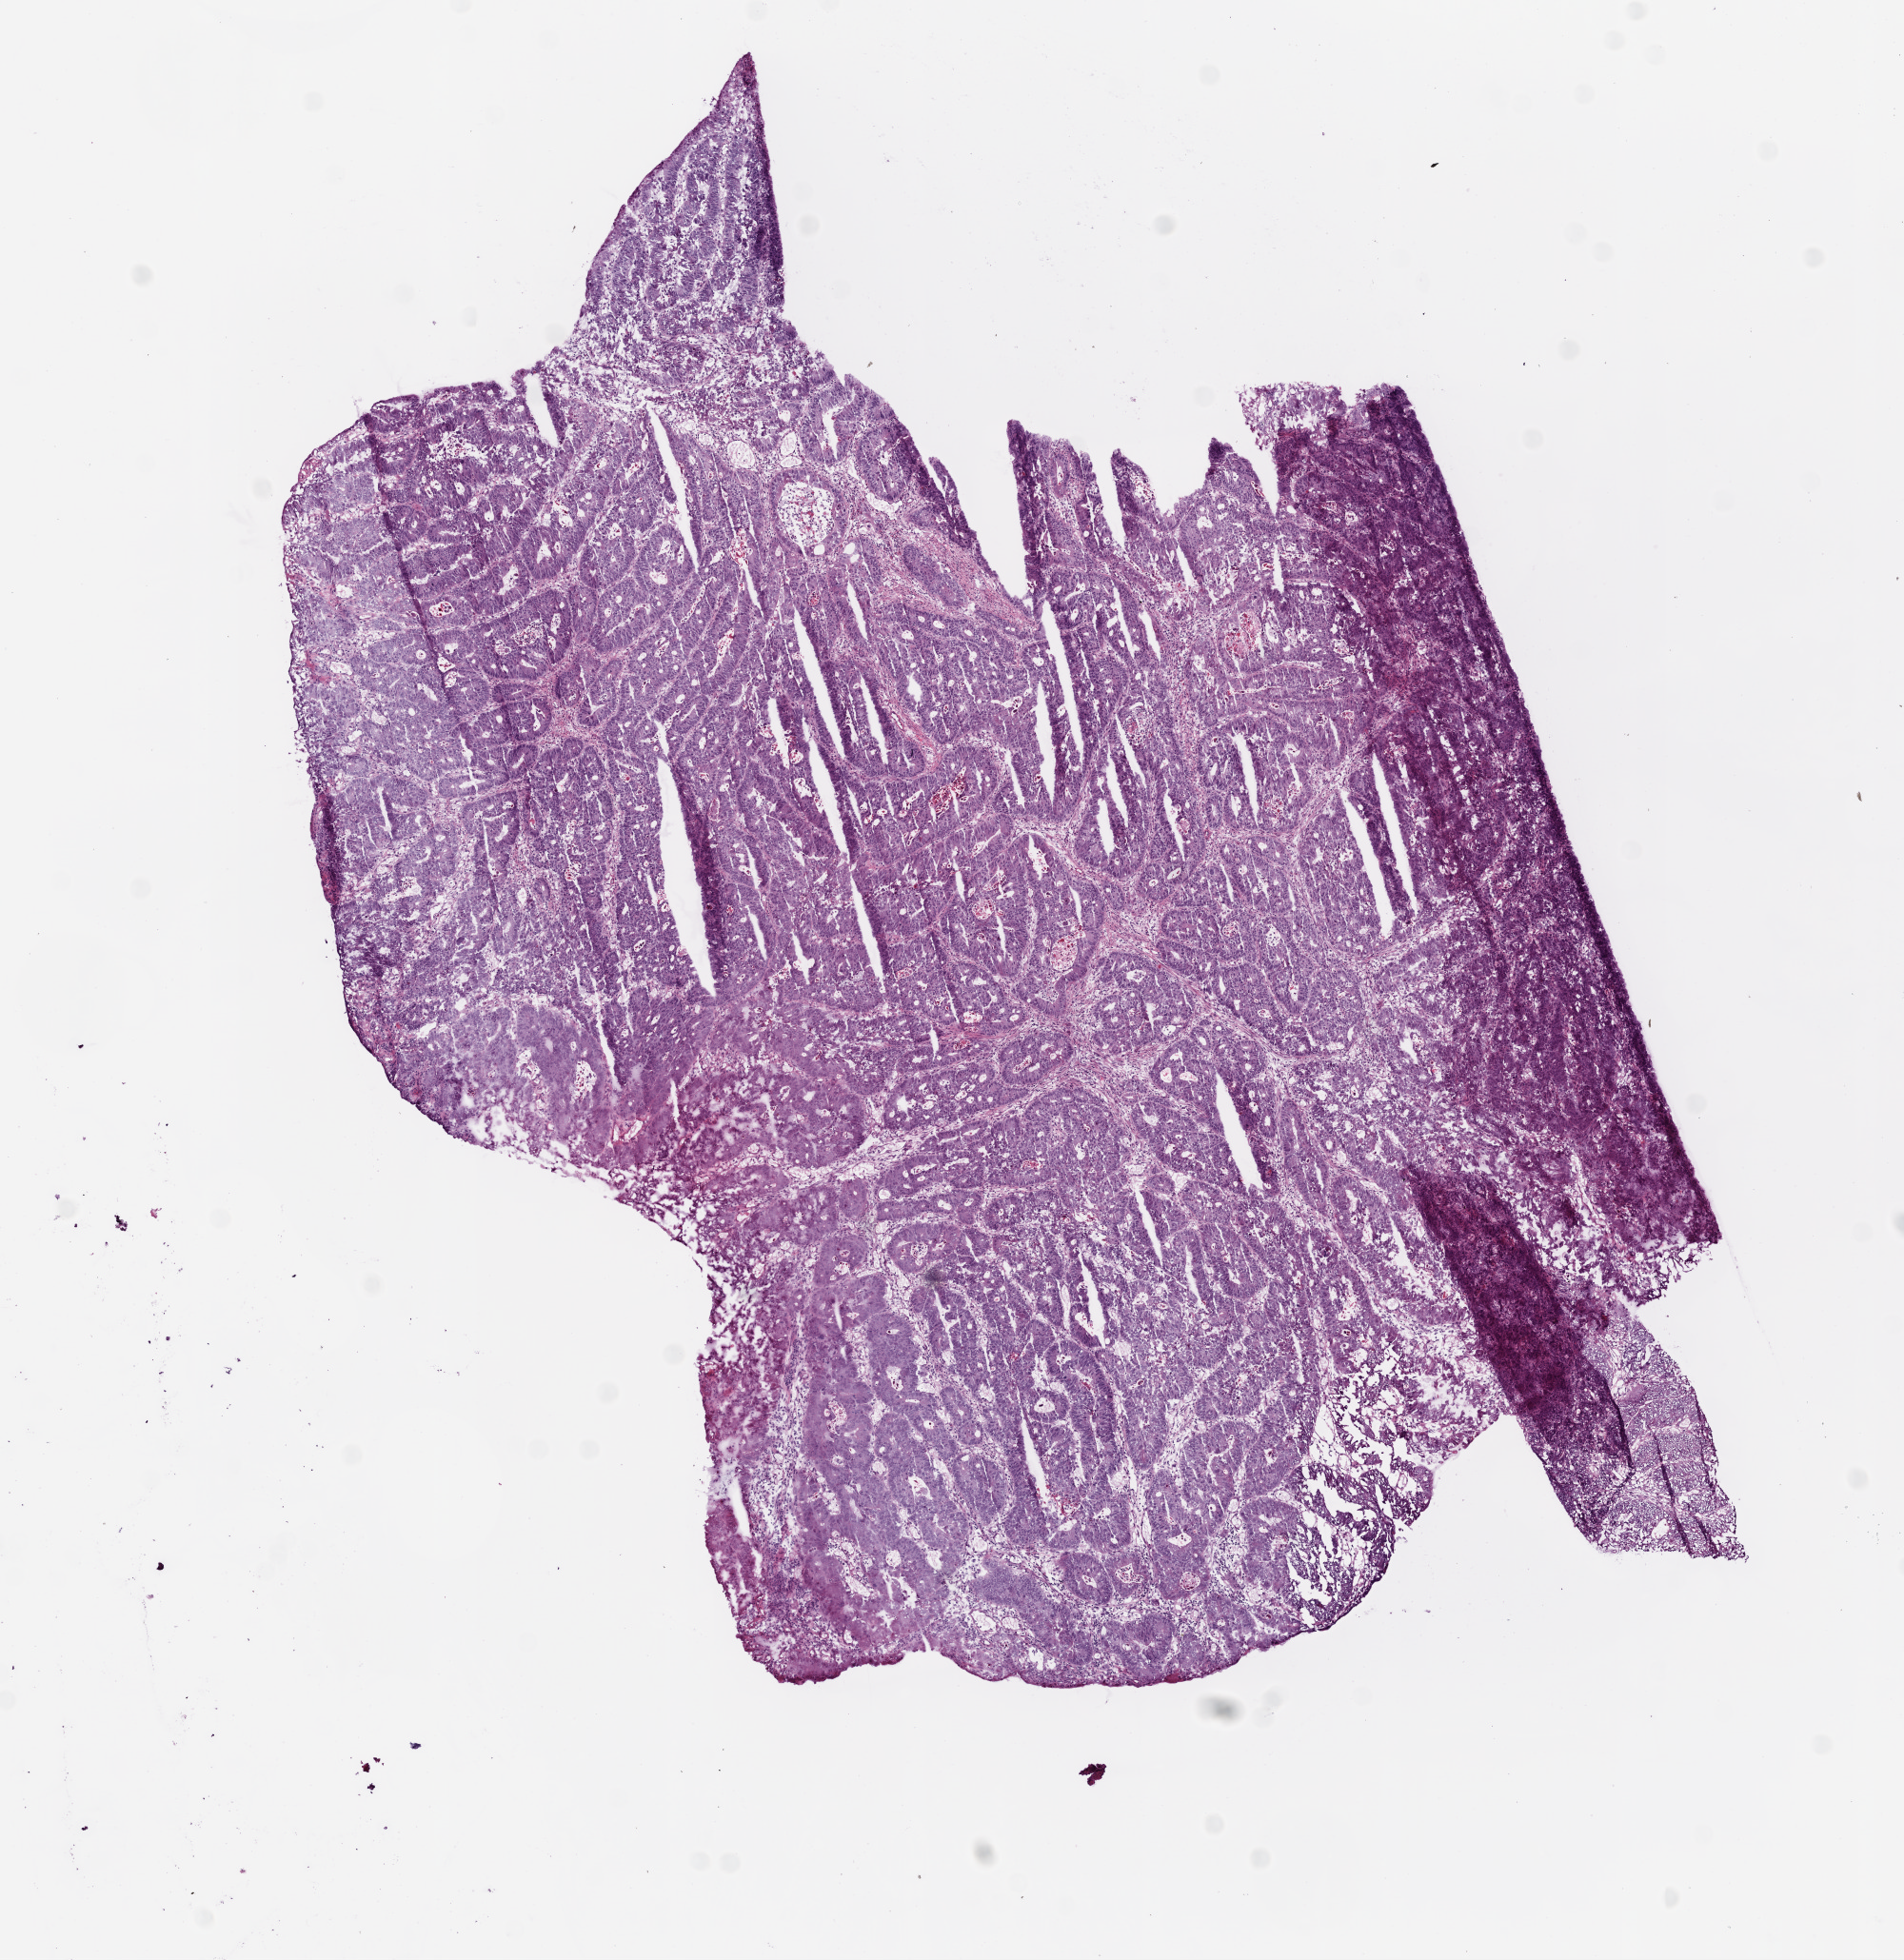
Digitized H&E tissue section (whole slide), low-resolution overview of the scanned area, about 8.0 x 8.3 mm. Frozen section. Rectum, primary tumour sample. Female, age 63 years at initial diagnosis. Composition of this section per pathologist review: tumour cells 87%, tumour nuclei 75%, normal cells 0%, stromal cells 10%, necrosis 3%.
AJCC pathologic stage: I. Histologic diagnosis: Adenocarcinoma, NOS. Lymph nodes positive (case pathology): 0 of 34 examined.